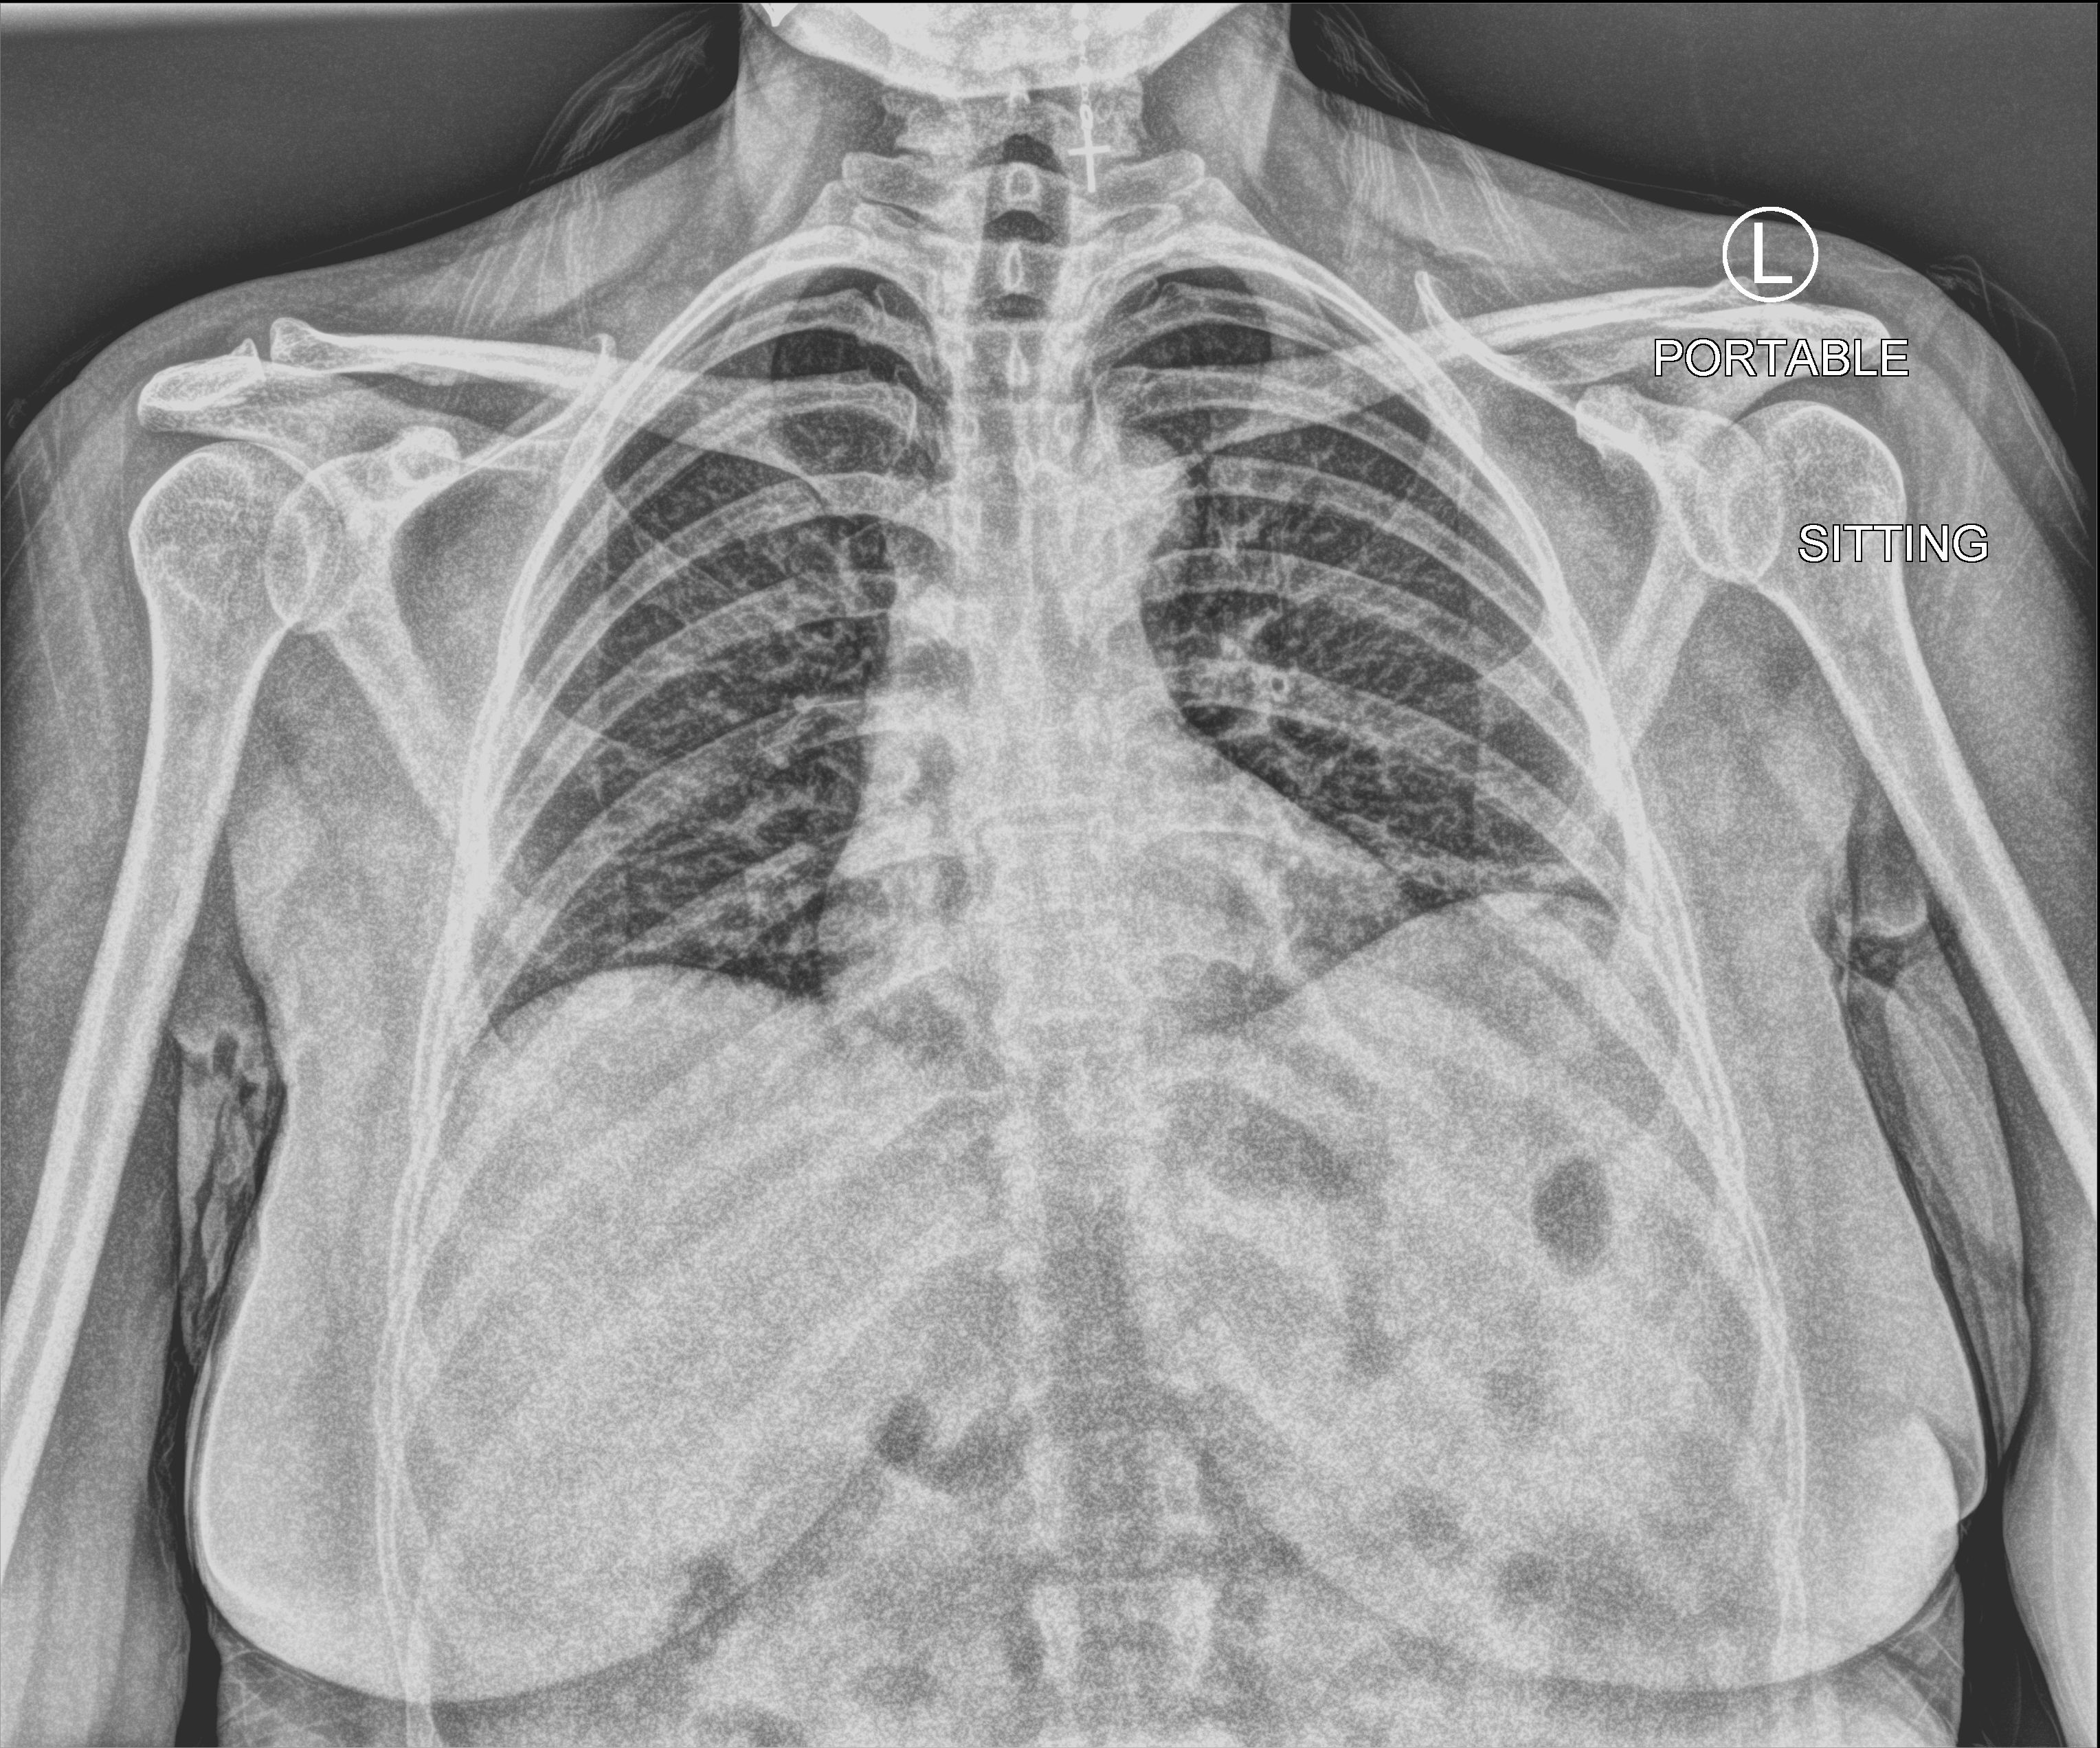
Chest X-ray (portable). Patient hospitalised with COVID-19; female, aged 18–59 years.
From the hospital-stay record, not from the radiograph (when in the stay this image was taken is not recorded):
- mechanically ventilated during this hospital stay: no
- smoking status (admission record): never